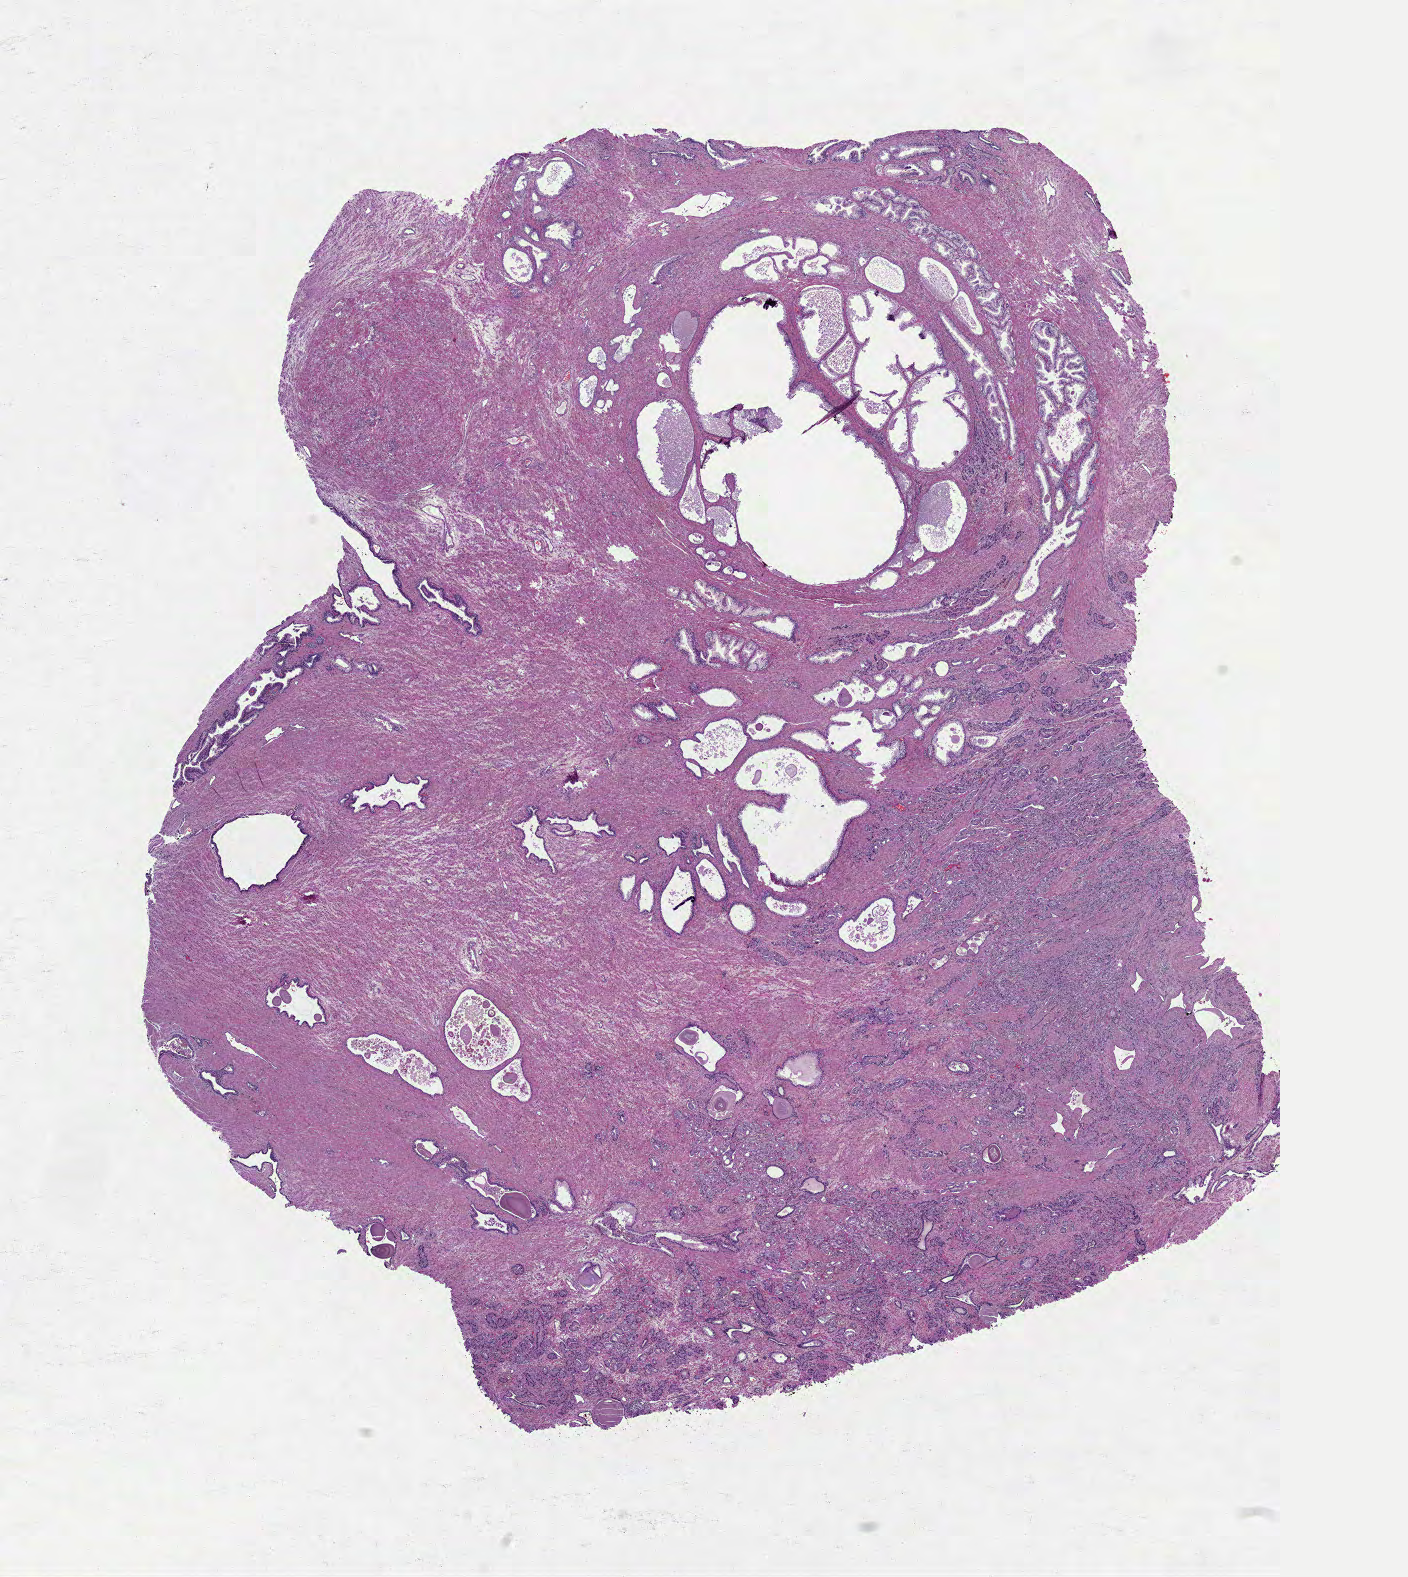
H&E whole-slide image, shown as a low-resolution overview of the whole scanned area (about 11.4 x 12.7 mm, from a 40x scan). Formalin-fixed paraffin-embedded (FFPE) diagnostic section. Primary tumour sample from the prostate. Patient: male, age at initial diagnosis 61 years. Gleason score: 7 (3+4).
Pathologic diagnosis: Adenocarcinoma, NOS (prostate gland). Laterality: left. Lymph nodes positive (case pathology): 0 of 10 examined.